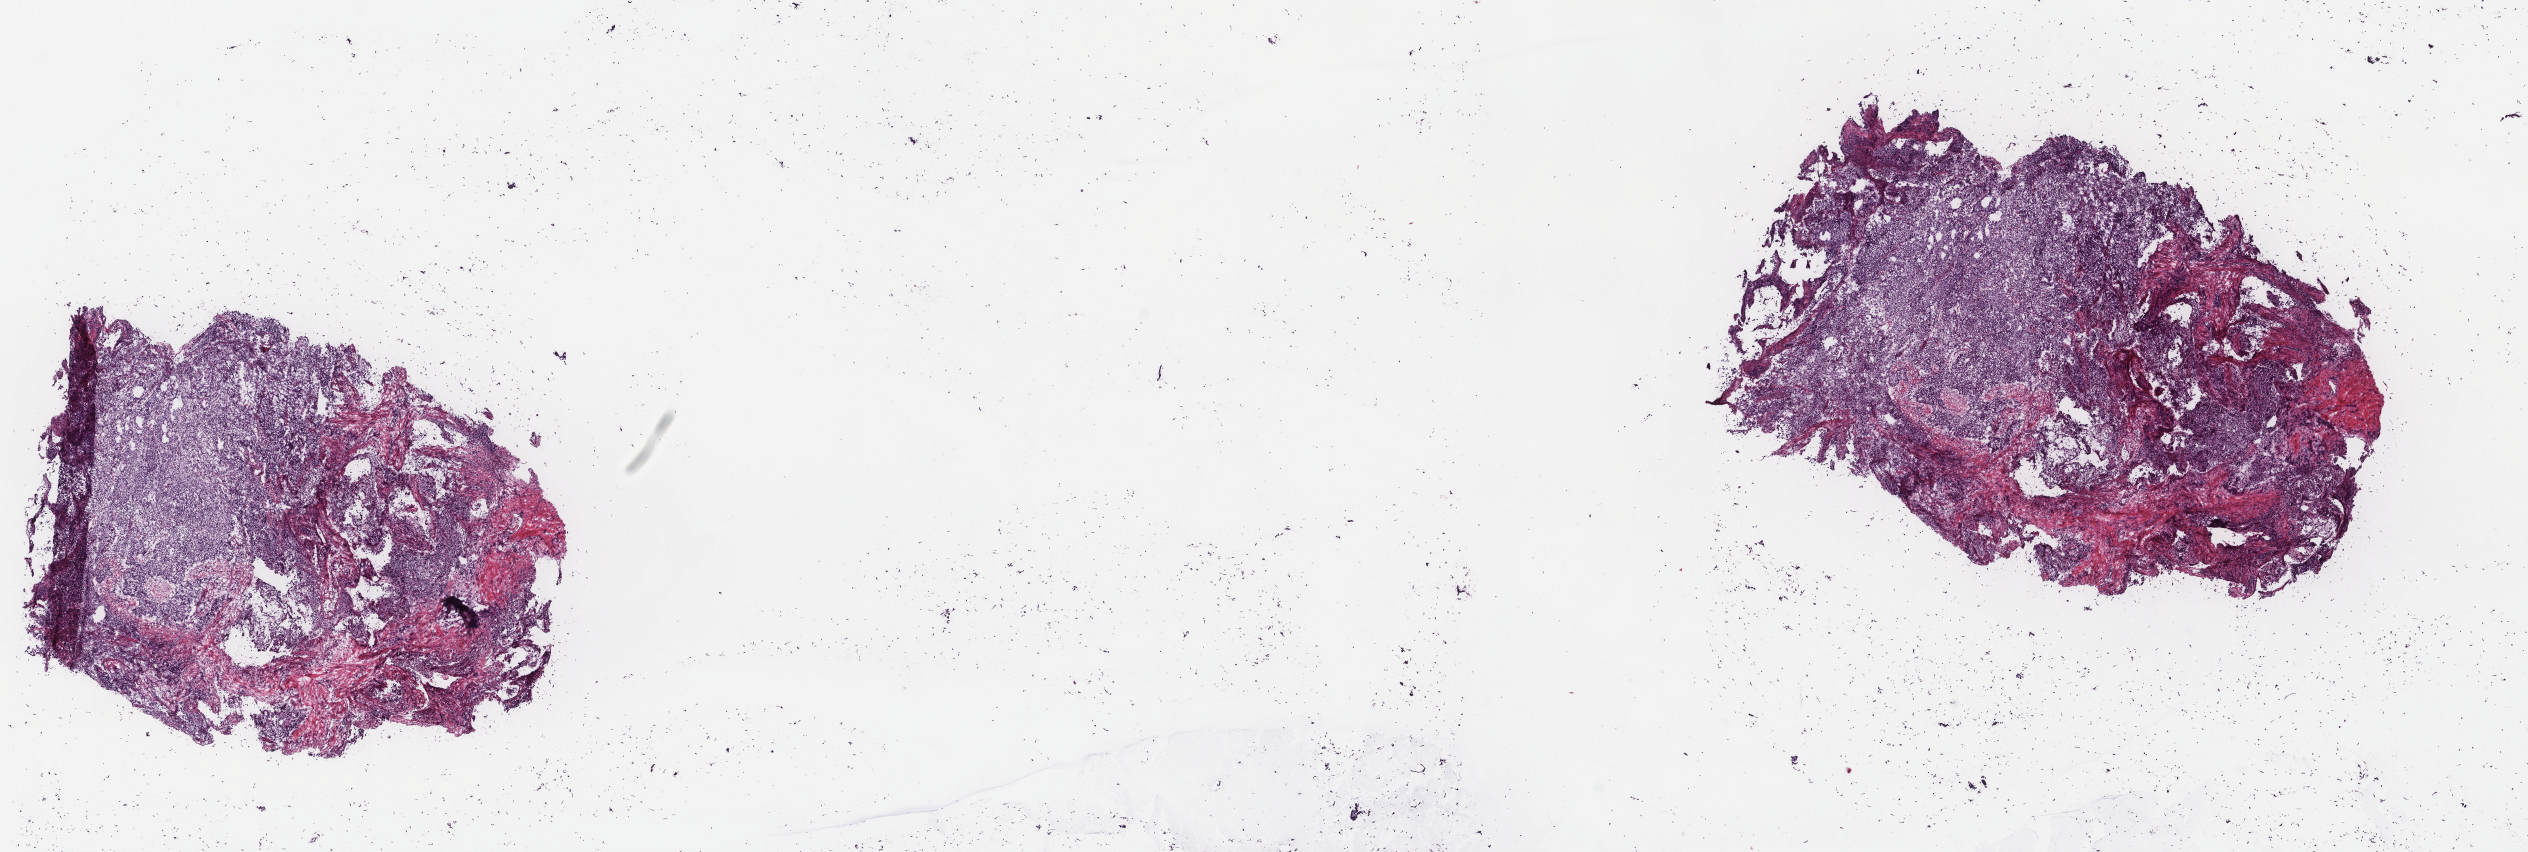
Whole-slide histology image, H&E-stained — a low-resolution overview of the entire scanned area, about 20.1 x 6.8 mm (acquisition: 40x scan); frozen section from the top of the tissue portion; sample: primary tumour, uterus. Female, age 69 years at initial diagnosis. Histologic grade: G3 (poorly differentiated). Composition of this section per pathologist review: tumour cells 70%, tumour nuclei 70%, normal cells 0%, stromal cells 20%, necrosis 10%. Inflammatory infiltration, as recorded: lymphocyte infiltration 40%, monocyte infiltration 20%, neutrophil infiltration 20%.
FIGO stage: IB. Histologic diagnosis: Endometrioid adenocarcinoma, NOS (endometrium).